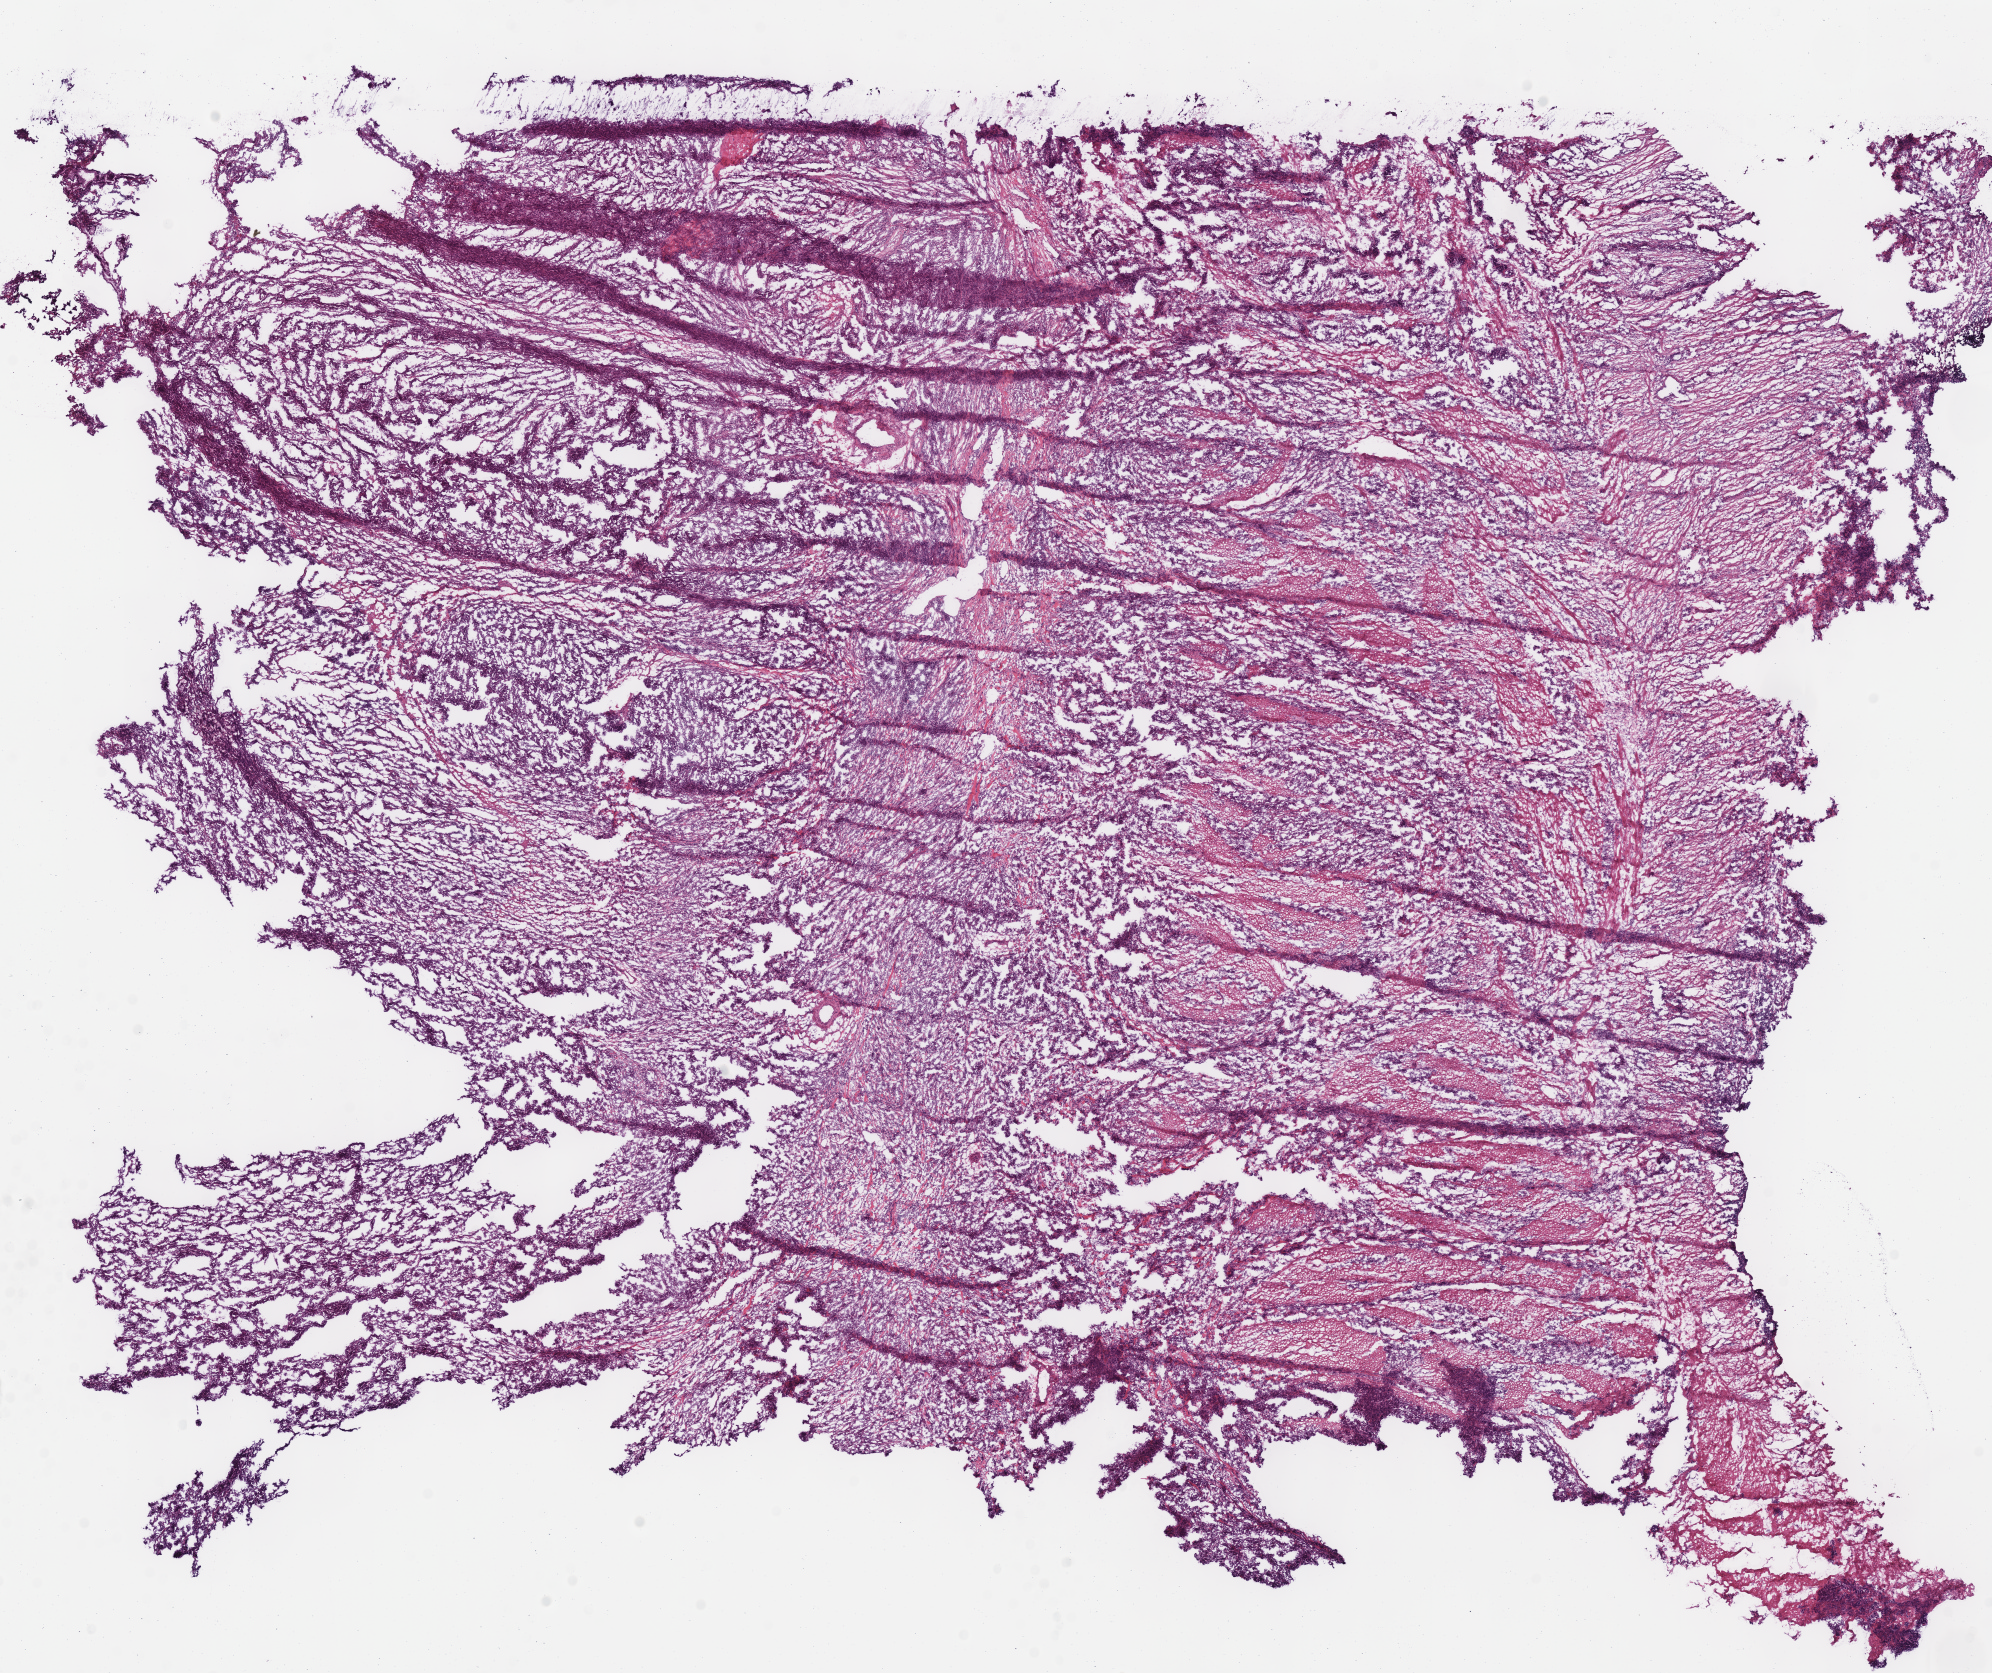
Hematoxylin and eosin (H&E) stained whole-slide image, low-resolution overview of the scanned area, about 15.7 x 13.2 mm (from a 40x scan); frozen section; stomach, primary tumour sample. Male, age 51 years at initial diagnosis. Histologic grade: G3 (poorly differentiated). Composition of this section per pathologist review: tumour cells 100%, tumour nuclei 70%, normal cells 0%, stromal cells 0%, necrosis 0%. Infiltration values recorded for this section: lymphocyte infiltration 15%, monocyte infiltration 5%, neutrophil infiltration 5%.
Histologic diagnosis: Adenocarcinoma, NOS (fundus of stomach). AJCC pathologic stage: IIB (7th edition). TNM: T3 N1 M0.